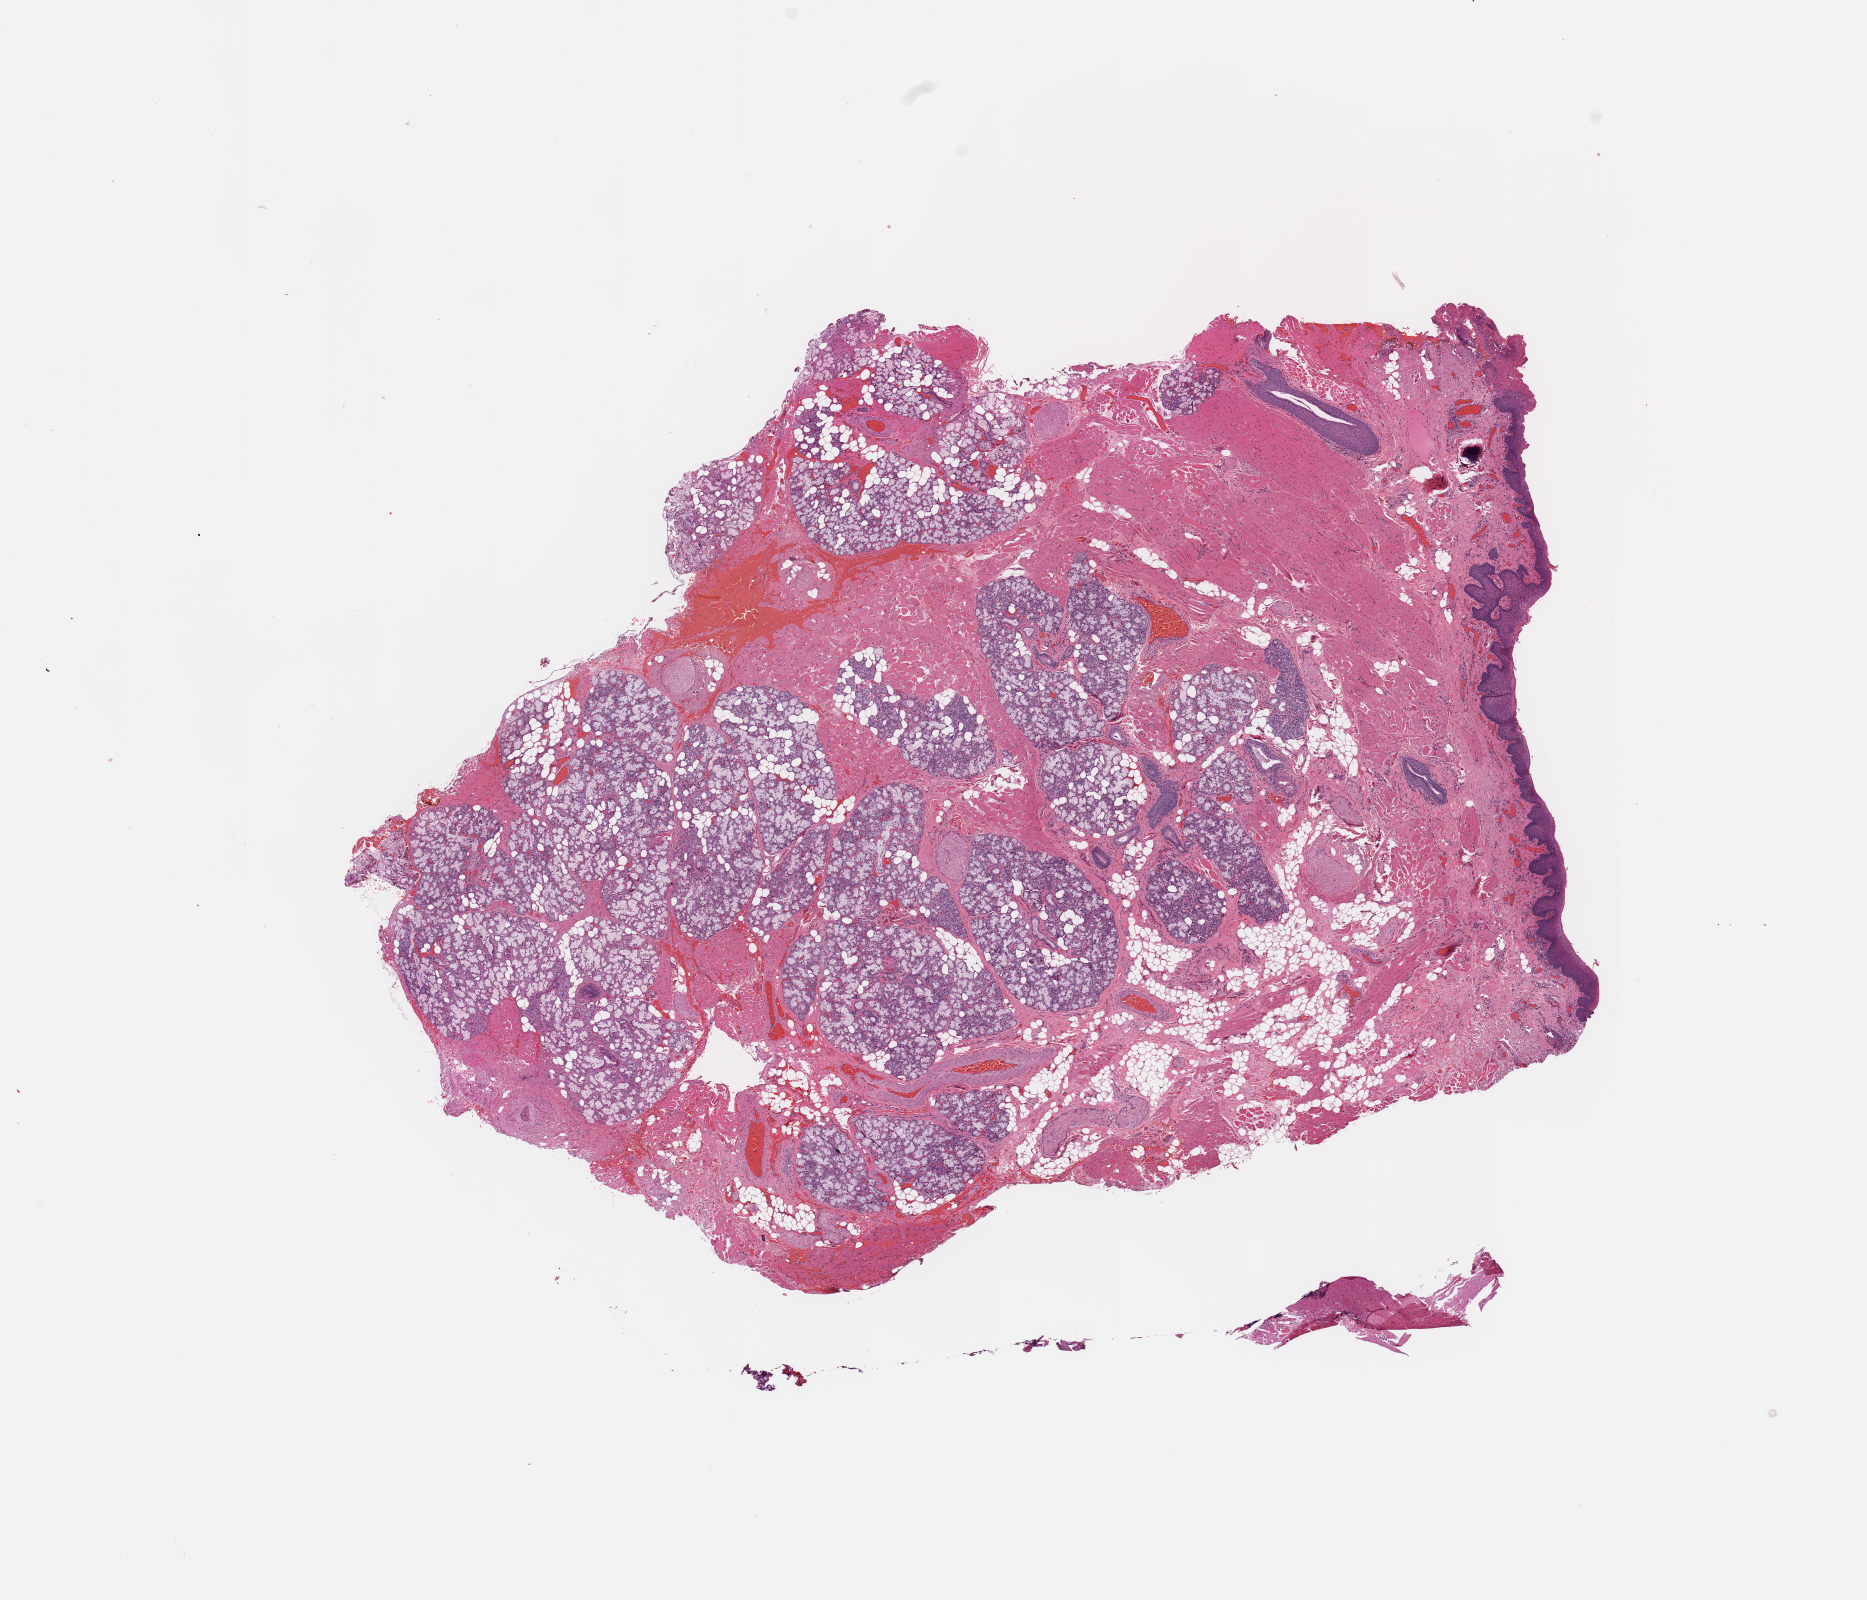
Digitized H&E-stained tissue section (whole slide) — low-resolution overview of the scanned area, about 14.8 x 12.7 mm (slide scanned at 20x). Normal (non-tumour) tissue sample, sampled site: floor of mouth. 56-year-old male patient.
- this section: normal (non-tumour) tissue from the same patient
- patient diagnosis: Squamous cell carcinoma, NOS (floor of mouth, NOS)